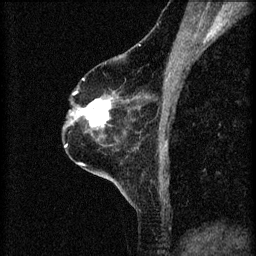
Breast MRI (dynamic contrast-enhanced), one sagittal slice. Slice 42 of 60 in the series (ordered by position). 3 images stored at this slice position (order not interpretable as contrast timing). 1.5 T. TE 4.2 ms, TR 8.2 ms. 2 mm slice thickness. 256 × 256 image matrix, field of view 180 × 180 mm. Female patient, age 60 years.
Structures marked on this image (semi-automatic segmentation, software-assisted and operator-edited):
- analysis volume of interest (the breast-tissue region the enhancement analysis was run in; not a lesion): bounding box [x1, y1, x2, y2] px = [78, 94, 114, 131]
- tumour enhancement mask (voxels above the 70 % enhancement threshold inside the analysis volume of interest): [78, 98, 112, 127]